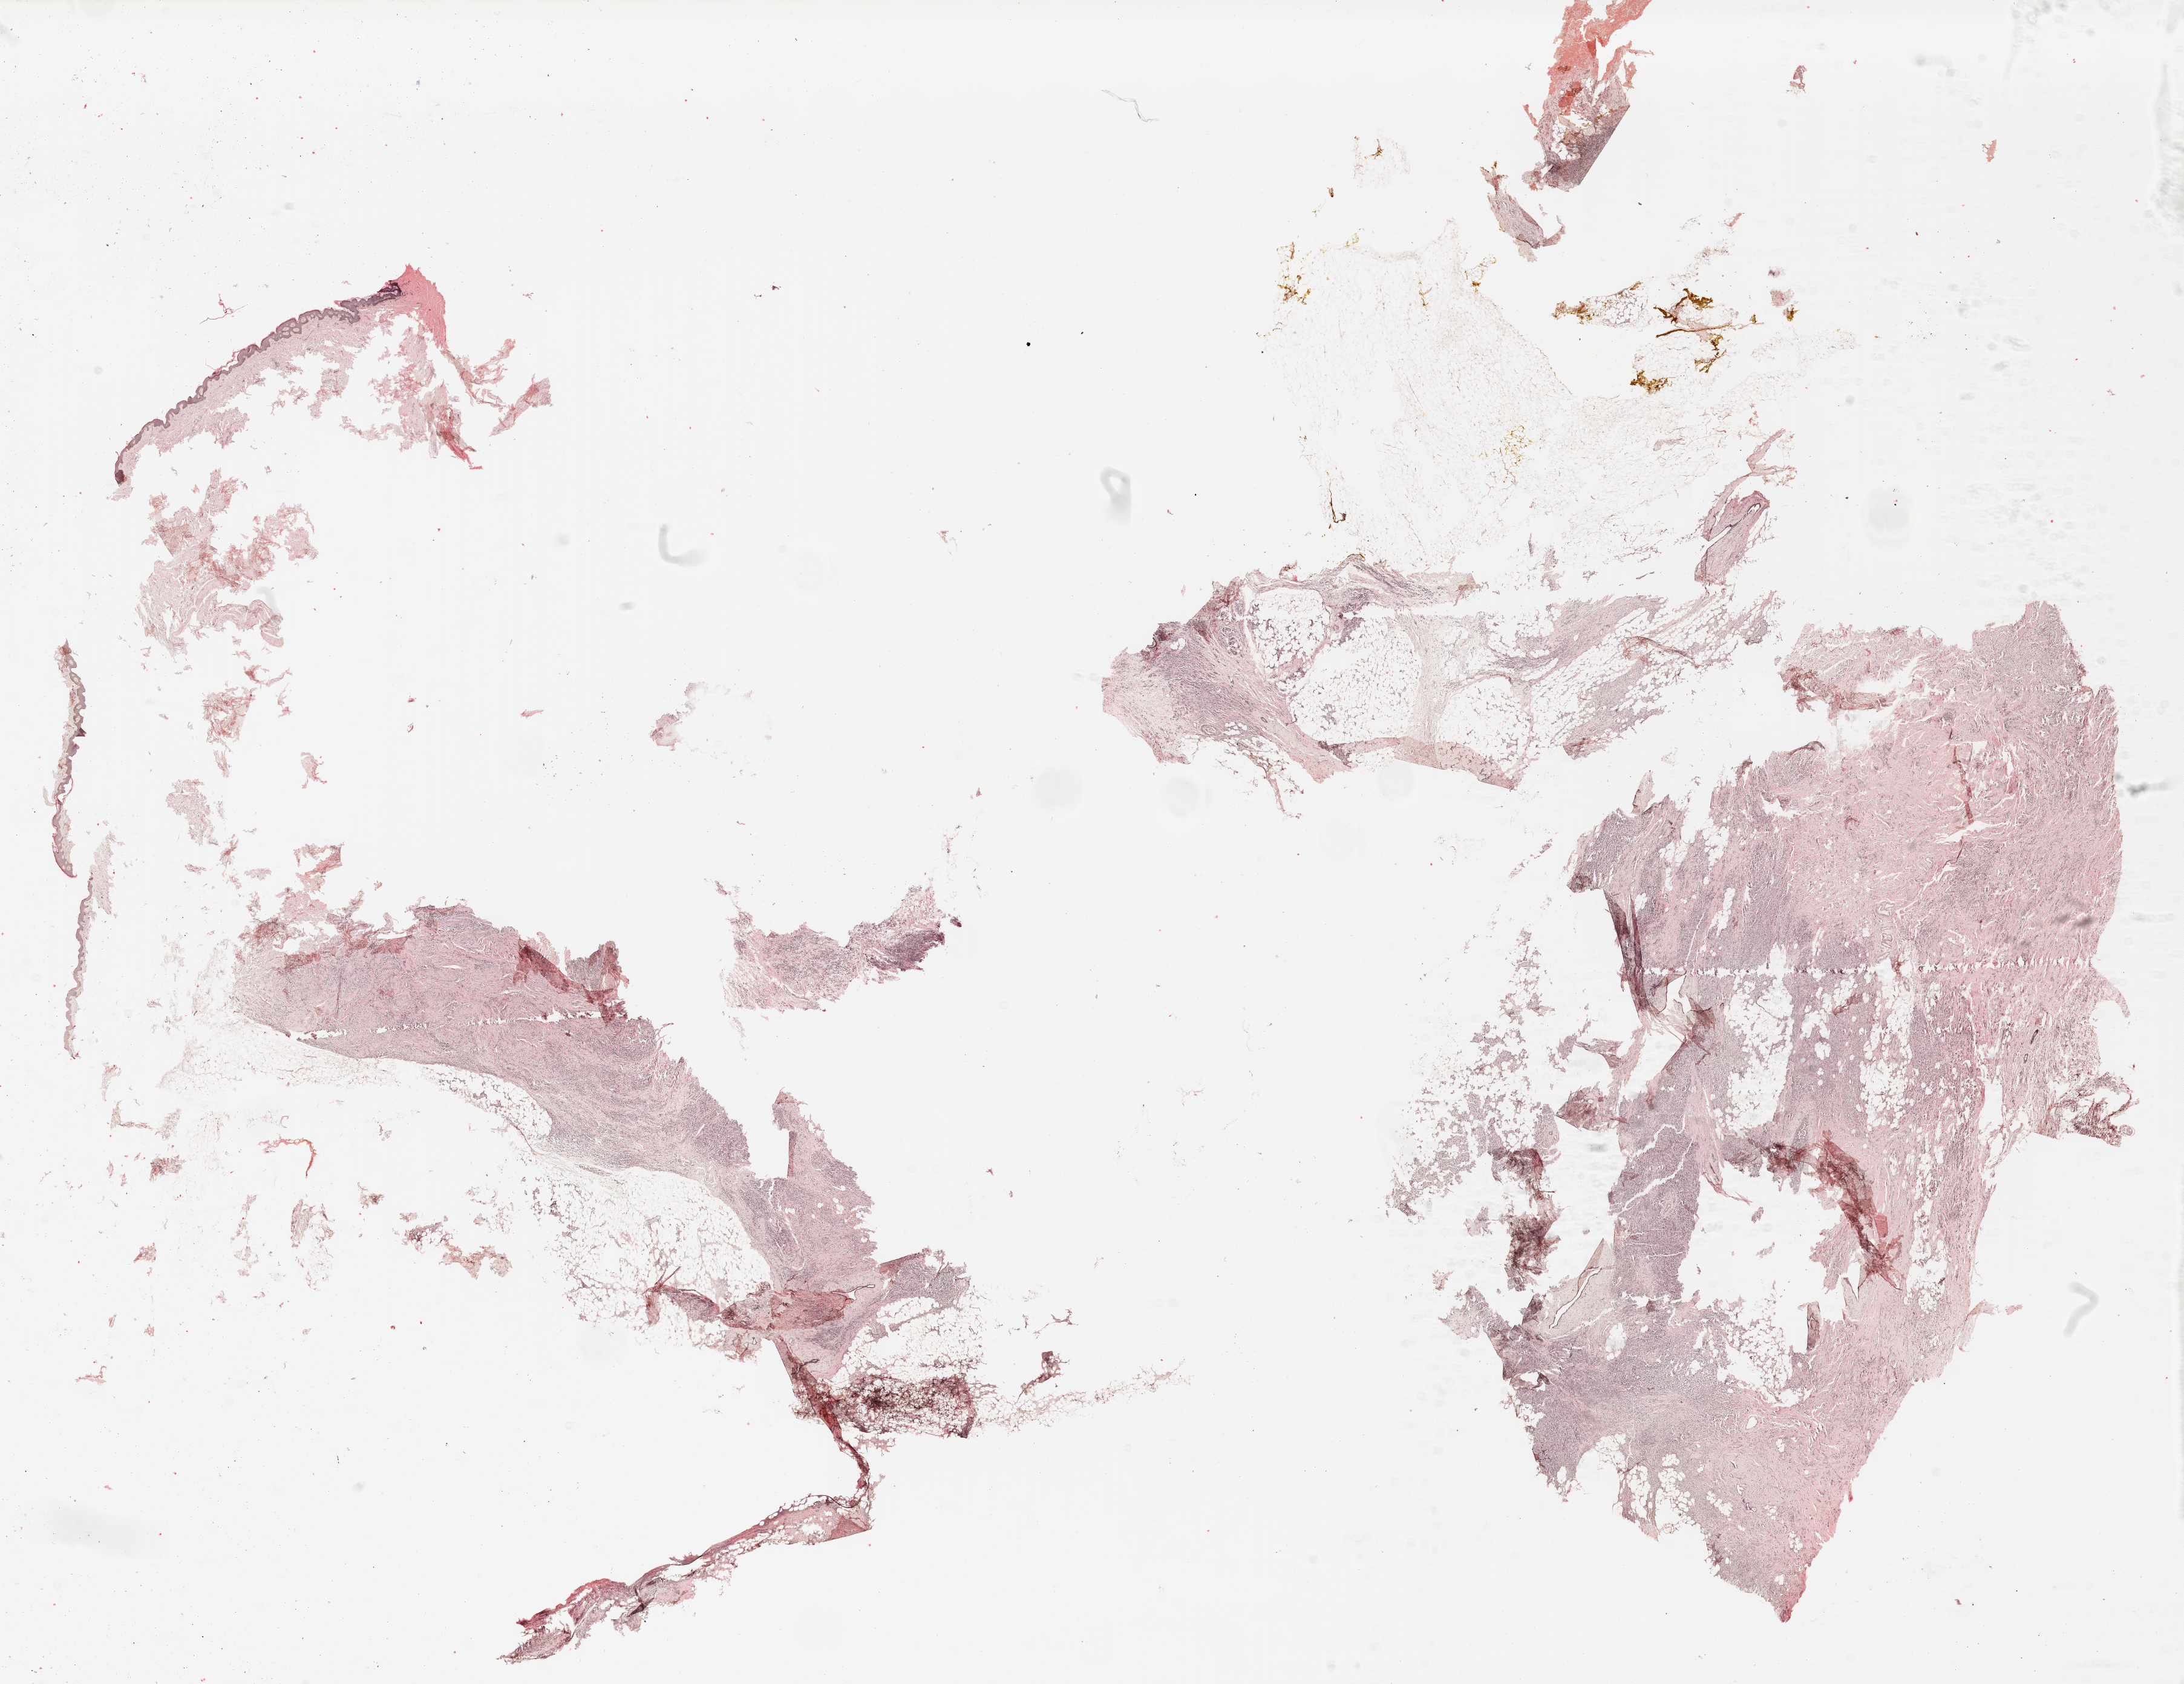
Whole-slide histology image, Hematoxylin and eosin (H&E) stained, low-resolution overview of the scanned area, about 28.8 x 22.2 mm. Formalin-fixed paraffin-embedded (FFPE) diagnostic section. Breast, primary tumour sample. Patient: female, age at initial diagnosis 51 years.
AJCC pathologic stage: IIB (6th edition). Histologic diagnosis: Lobular carcinoma, NOS.